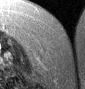
MRI of an extremity soft-tissue mass, one axial slice. Slice 10 of 46 in the series (ordered by position). T2-weighted fat-saturated. MR volume resampled by the dataset authors to the PET/CT grid (not the native acquisition matrix). 3.27 mm slice thickness. 85 × 89 image matrix. Female patient. From the clinical record (not read from this slice): histological type: leiomyosarcoma; grade: intermediate; site of the primary tumour: parascapusular.
Structures marked on this image (expert contour drawn on MRI and transferred to this co-registered scan by the dataset authors):
- gross tumour volume including surrounding oedema: bounding box (x1, y1, x2, y2) in pixels: (41, 57, 49, 63)